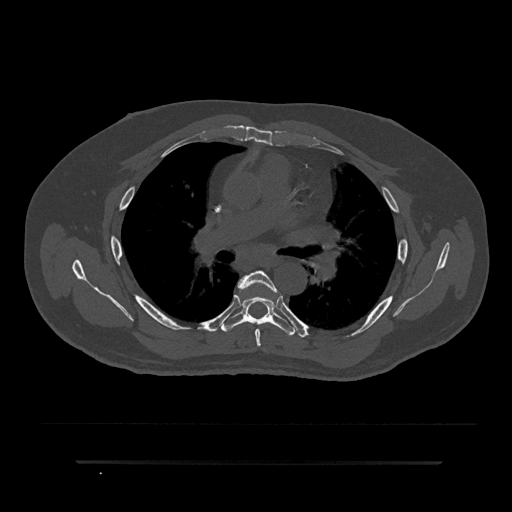
CT including the spine, one axial slice; slice 546 of 797 in the series (ordered by position); reconstruction kernel Br40s/3; bone window (W 1800 / L 400 HU); 512 × 512 image matrix. Male patient, age 59 years. Case-level facts recorded for this patient, not image findings: primary cancer: bile ducts; vertebrae with lytic lesions (as recorded): T10.
Outlined on this slice (semi-automatically segmented with operator editing):
- T5 vertebra: bounding box <238,271,277,347> (left, top, right, bottom; pixels)
- T6 vertebra: <221,289,294,336>